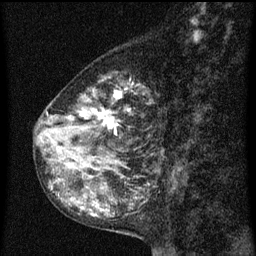
Breast MRI (dynamic contrast-enhanced), one sagittal slice; position 29 of 60 along the scan axis; dynamic contrast-enhanced series, image 2 of 3 at this slice position (ordered by acquisition); 1.5 T; TE 4.2 ms, TR 8 ms; 2 mm slice thickness; 256 × 256 image matrix, field of view 180 × 180 mm. Patient: female, 55 years.
Outlined on this slice (semi-automatically segmented with operator editing):
- analysis volume of interest (the breast-tissue region the enhancement analysis was run in; not a lesion): bounding box (x1, y1, x2, y2) in pixels: (36, 74, 157, 151)
- tumour enhancement mask (voxels above the 70 % enhancement threshold inside the analysis volume of interest): (46, 80, 133, 149)